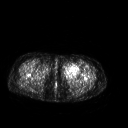
FDG PET of an extremity soft-tissue mass (from a PET/CT study), one axial slice. 128 × 128 image matrix, field of view 500 × 500 mm. Female patient, age 42 years. Case-level facts recorded for this patient, not image findings: histological type: pleiomorphic leiomyosarcoma; grade: intermediate; site of the primary tumour: left thigh.
Outlined on this slice (expert contour drawn on MRI and transferred to this co-registered scan by the dataset authors):
- gross tumour volume including surrounding oedema: bounding box <62,63,80,79> (left, top, right, bottom; pixels)
- gross tumour volume (mass): <62,63,80,79>